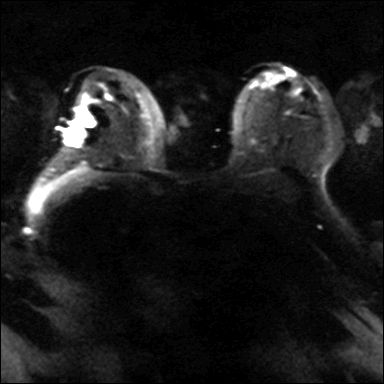
Breast MRI, one axial slice. Slice 24 of 42 in the series (ordered by position). Diffusion-weighted series; image 2 of 4 stored at this slice position (different b-values; order by instance number). 3 T. 4 mm slice thickness. 384 × 384 image matrix. Female patient.
Annotated regions visible in this slice (manually delineated by an expert):
- tumour on diffusion-weighted imaging: bounding box (x1, y1, x2, y2) in pixels: (68, 113, 95, 144)